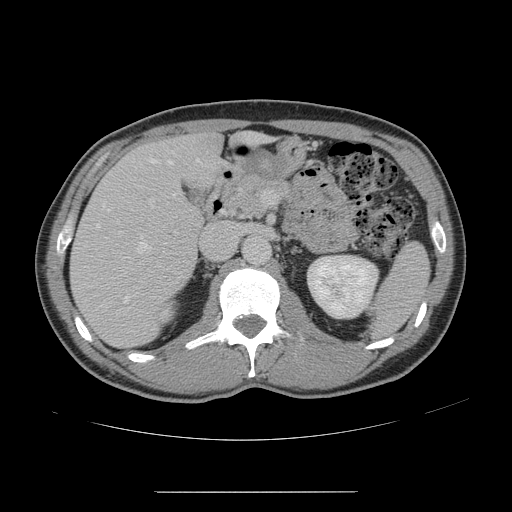
Contrast-enhanced abdominal CT, one axial slice. Slice 81 of 178 in the series (ordered by position). 120 kVp. Intravenous contrast given. Soft-tissue window (W 400 / L 40 HU). 2.5 mm slice thickness. 512 × 512 image matrix, field of view 401 × 401 mm. Male patient, age 53 years. Case-level facts recorded for this patient, not image findings: diagnosis: colorectal cancer liver metastases, imaged before liver resection; multiple liver metastases: yes.
Annotated regions visible in this slice (outlined manually by an expert reader):
- hepatic veins: bounding box (x1, y1, x2, y2) in pixels: (96, 158, 199, 303)
- liver: (71, 134, 257, 347)
- planned liver remnant (the part of the liver to remain after resection): (159, 134, 260, 180)
- portal vein (with intrahepatic branches): (149, 191, 267, 268)